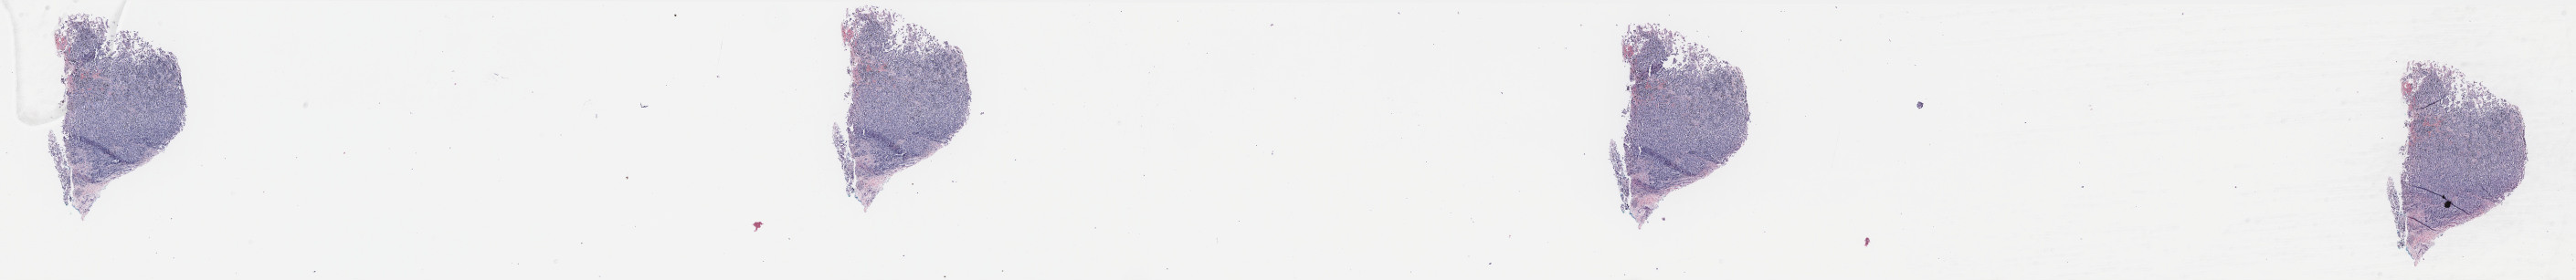
Digitized Hematoxylin and eosin (H&E) stained tissue section (whole slide) — a low-resolution overview of the entire scanned area, about 45.2 x 4.9 mm (from a 40x scan), FFPE section, primary tumour sample from the skin. Male, age 51 years at initial diagnosis.
Pathologic diagnosis: Malignant melanoma, NOS.